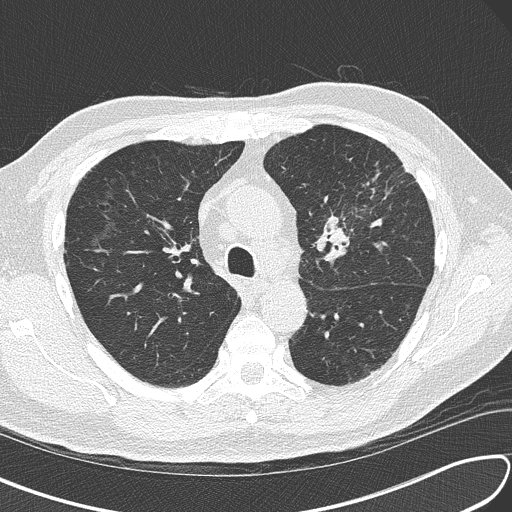
Axial slice from a low-dose chest CT screening exam; third screening round (two years after baseline); lung window (W 1500 / L -600 HU); lung (sharp) reconstruction kernel (B50f); slice 50 of 156 in the series; 512 × 512 image matrix. Male, age 67 years at enrolment.
Expert-annotated lung lesion, box from (x=299, y=180) to (x=400, y=277) px. Reader record for this screening exam (exam-level; its link to the box is not recorded): non-calcified nodule or mass ≥4 mm, left upper lobe, 30 × 23 mm, soft tissue attenuation, pre-existing on the prior screen: no. Participant outcome: lung cancer diagnosed 41 days after this screen — small cell carcinoma, NOS, left upper lobe, stage IV (AJCC 6th edition), 30 mm at pathology.